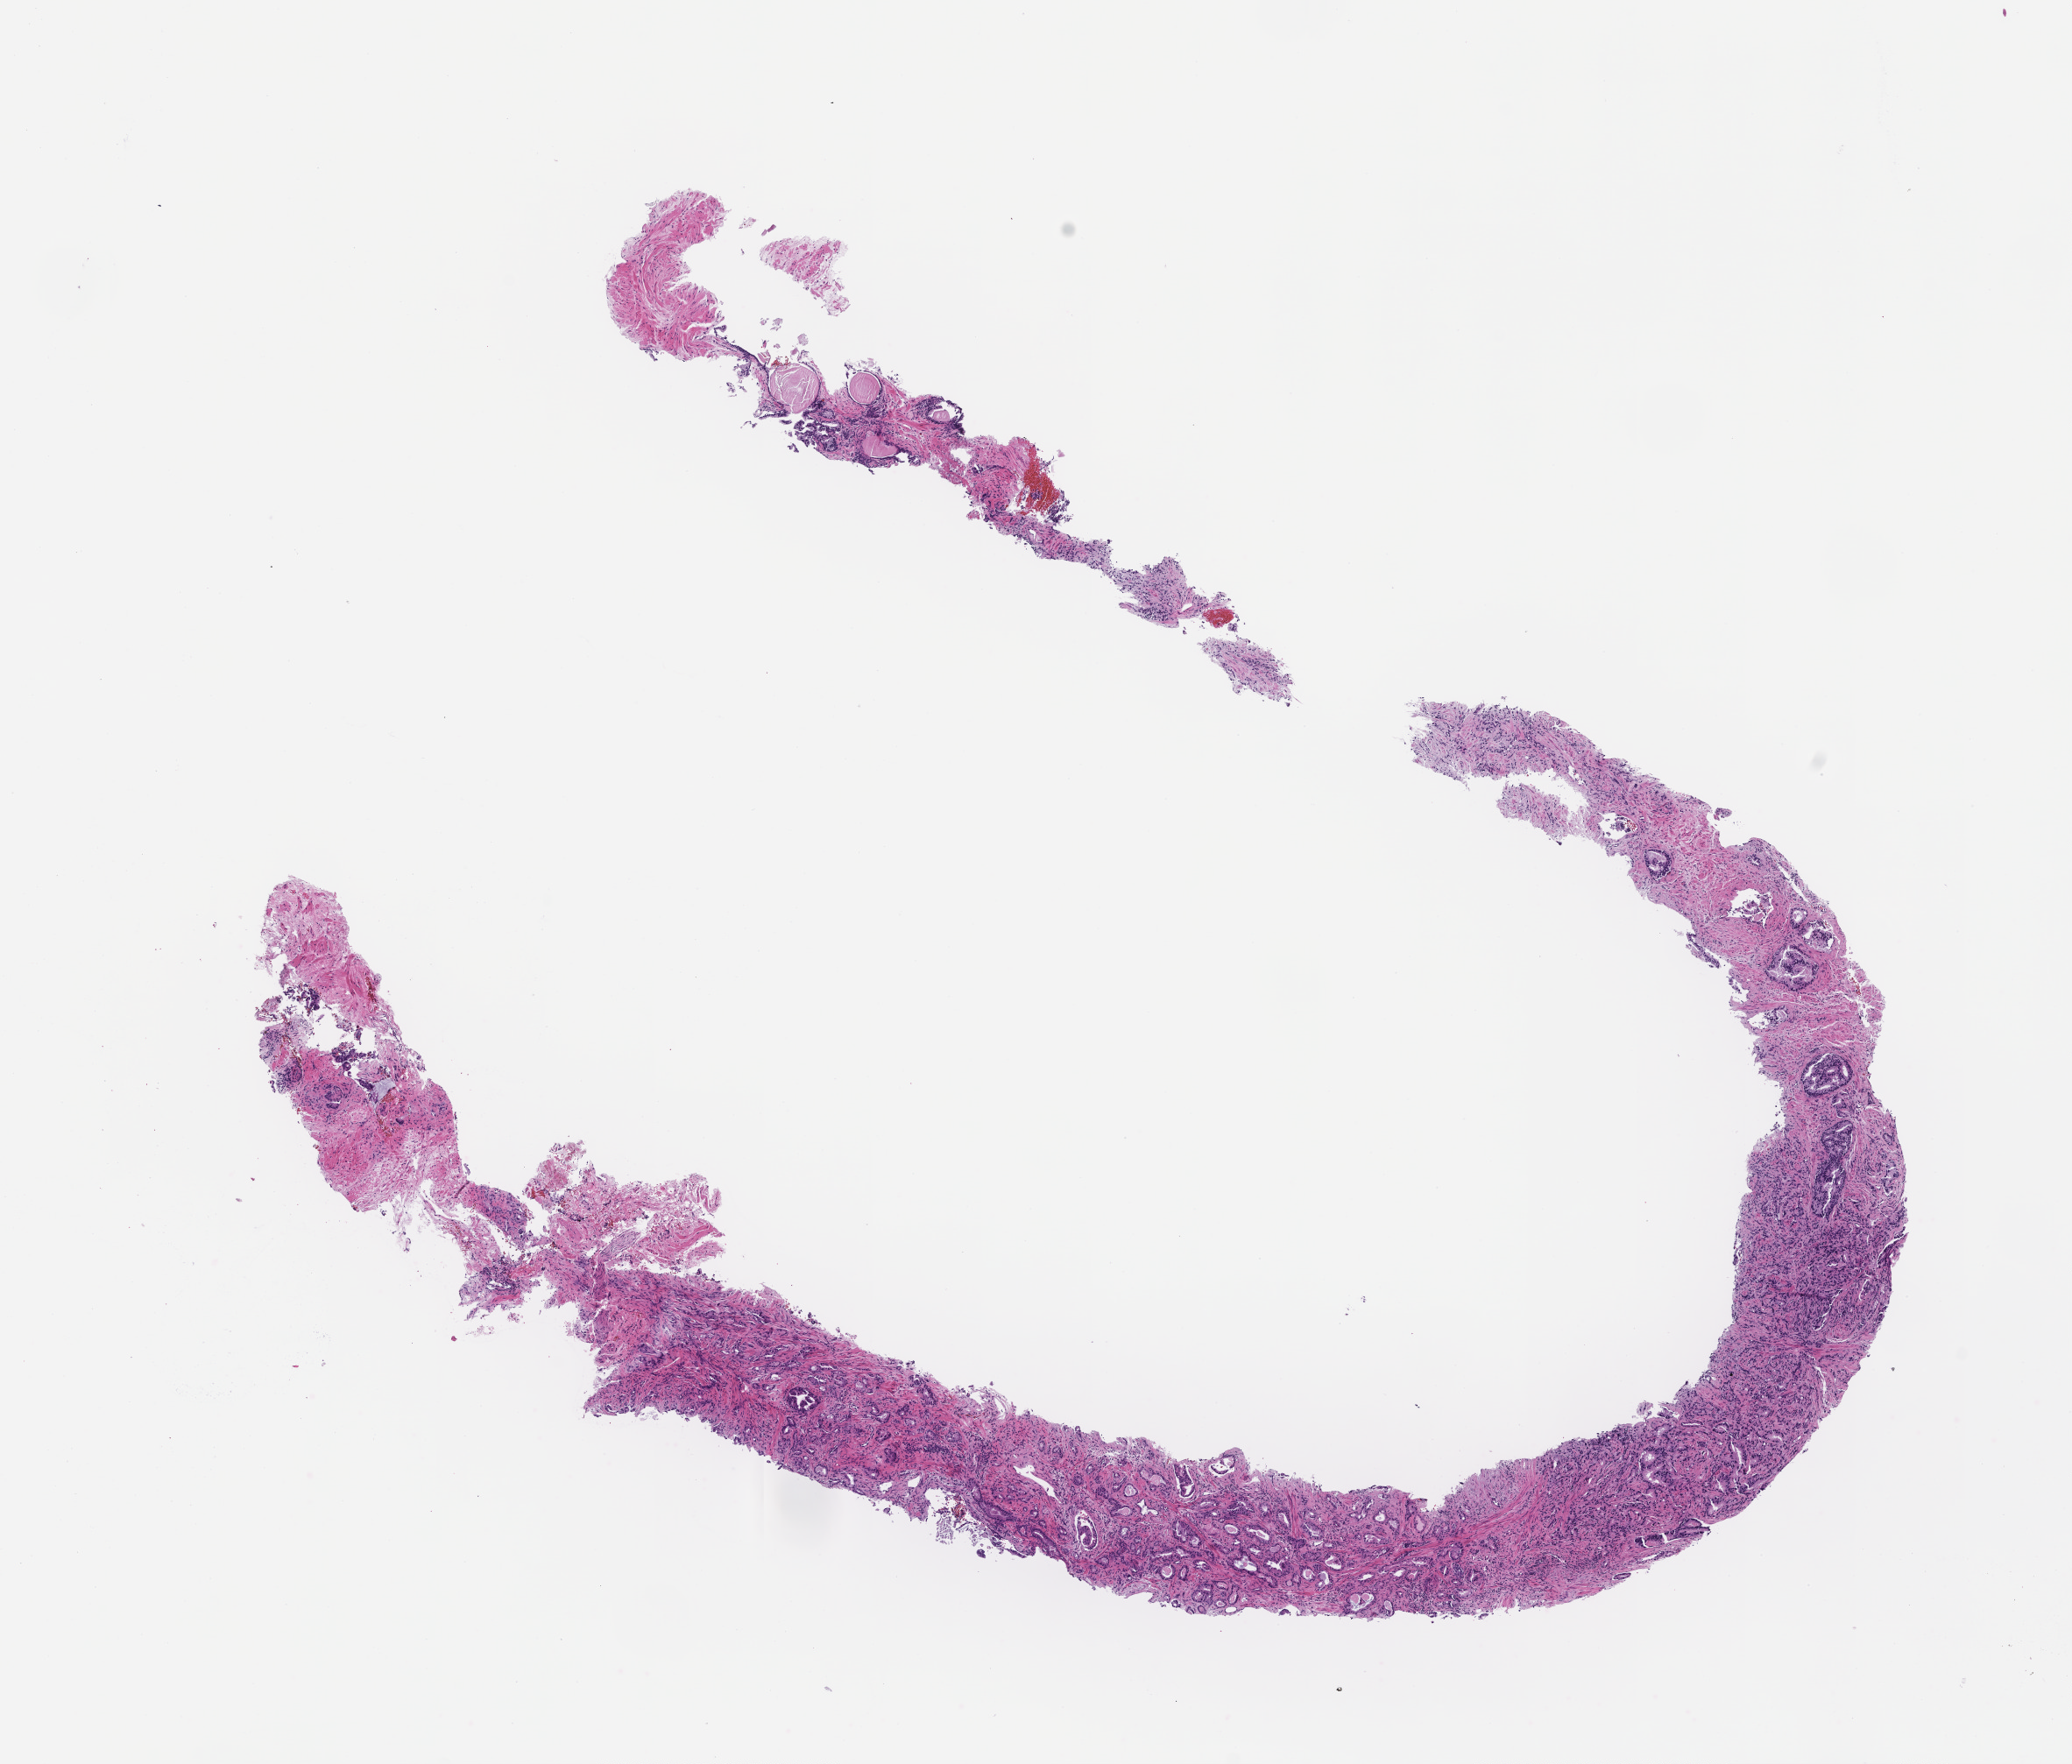
Haematoxylin and eosin whole-slide image, whole scanned area (about 9.5 x 8.1 mm) shown as a low-resolution overview. Formalin-fixed paraffin-embedded section. Site: prostate. Patient: male.
• this section: primary tumour tissue
• diagnosis: Prostate Carcinoma